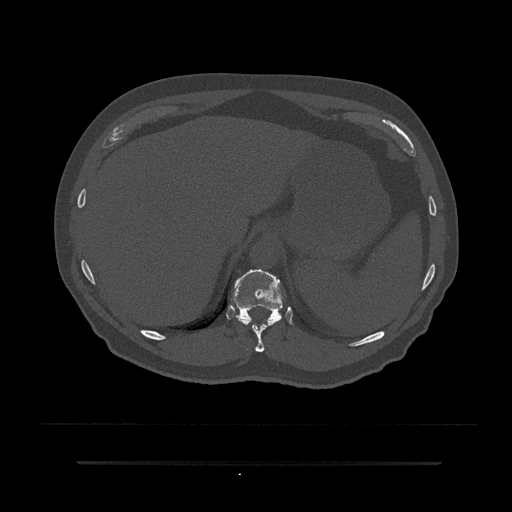
CT including the spine, one axial slice; position 296 of 797 along the scan axis; reconstruction kernel Br40s/3; bone window (W 1800 / L 400 HU); 0.5 mm slice thickness; 512 × 512 image matrix. Patient: male, 59 years. Case-level facts recorded for this patient, not image findings: primary cancer: bile ducts.
Annotated regions visible in this slice (semi-automatic segmentation, software-assisted and operator-edited):
- T10 vertebra: bounding box <236,317,282,352> (left, top, right, bottom; pixels)
- T11 vertebra: <229,269,288,322>